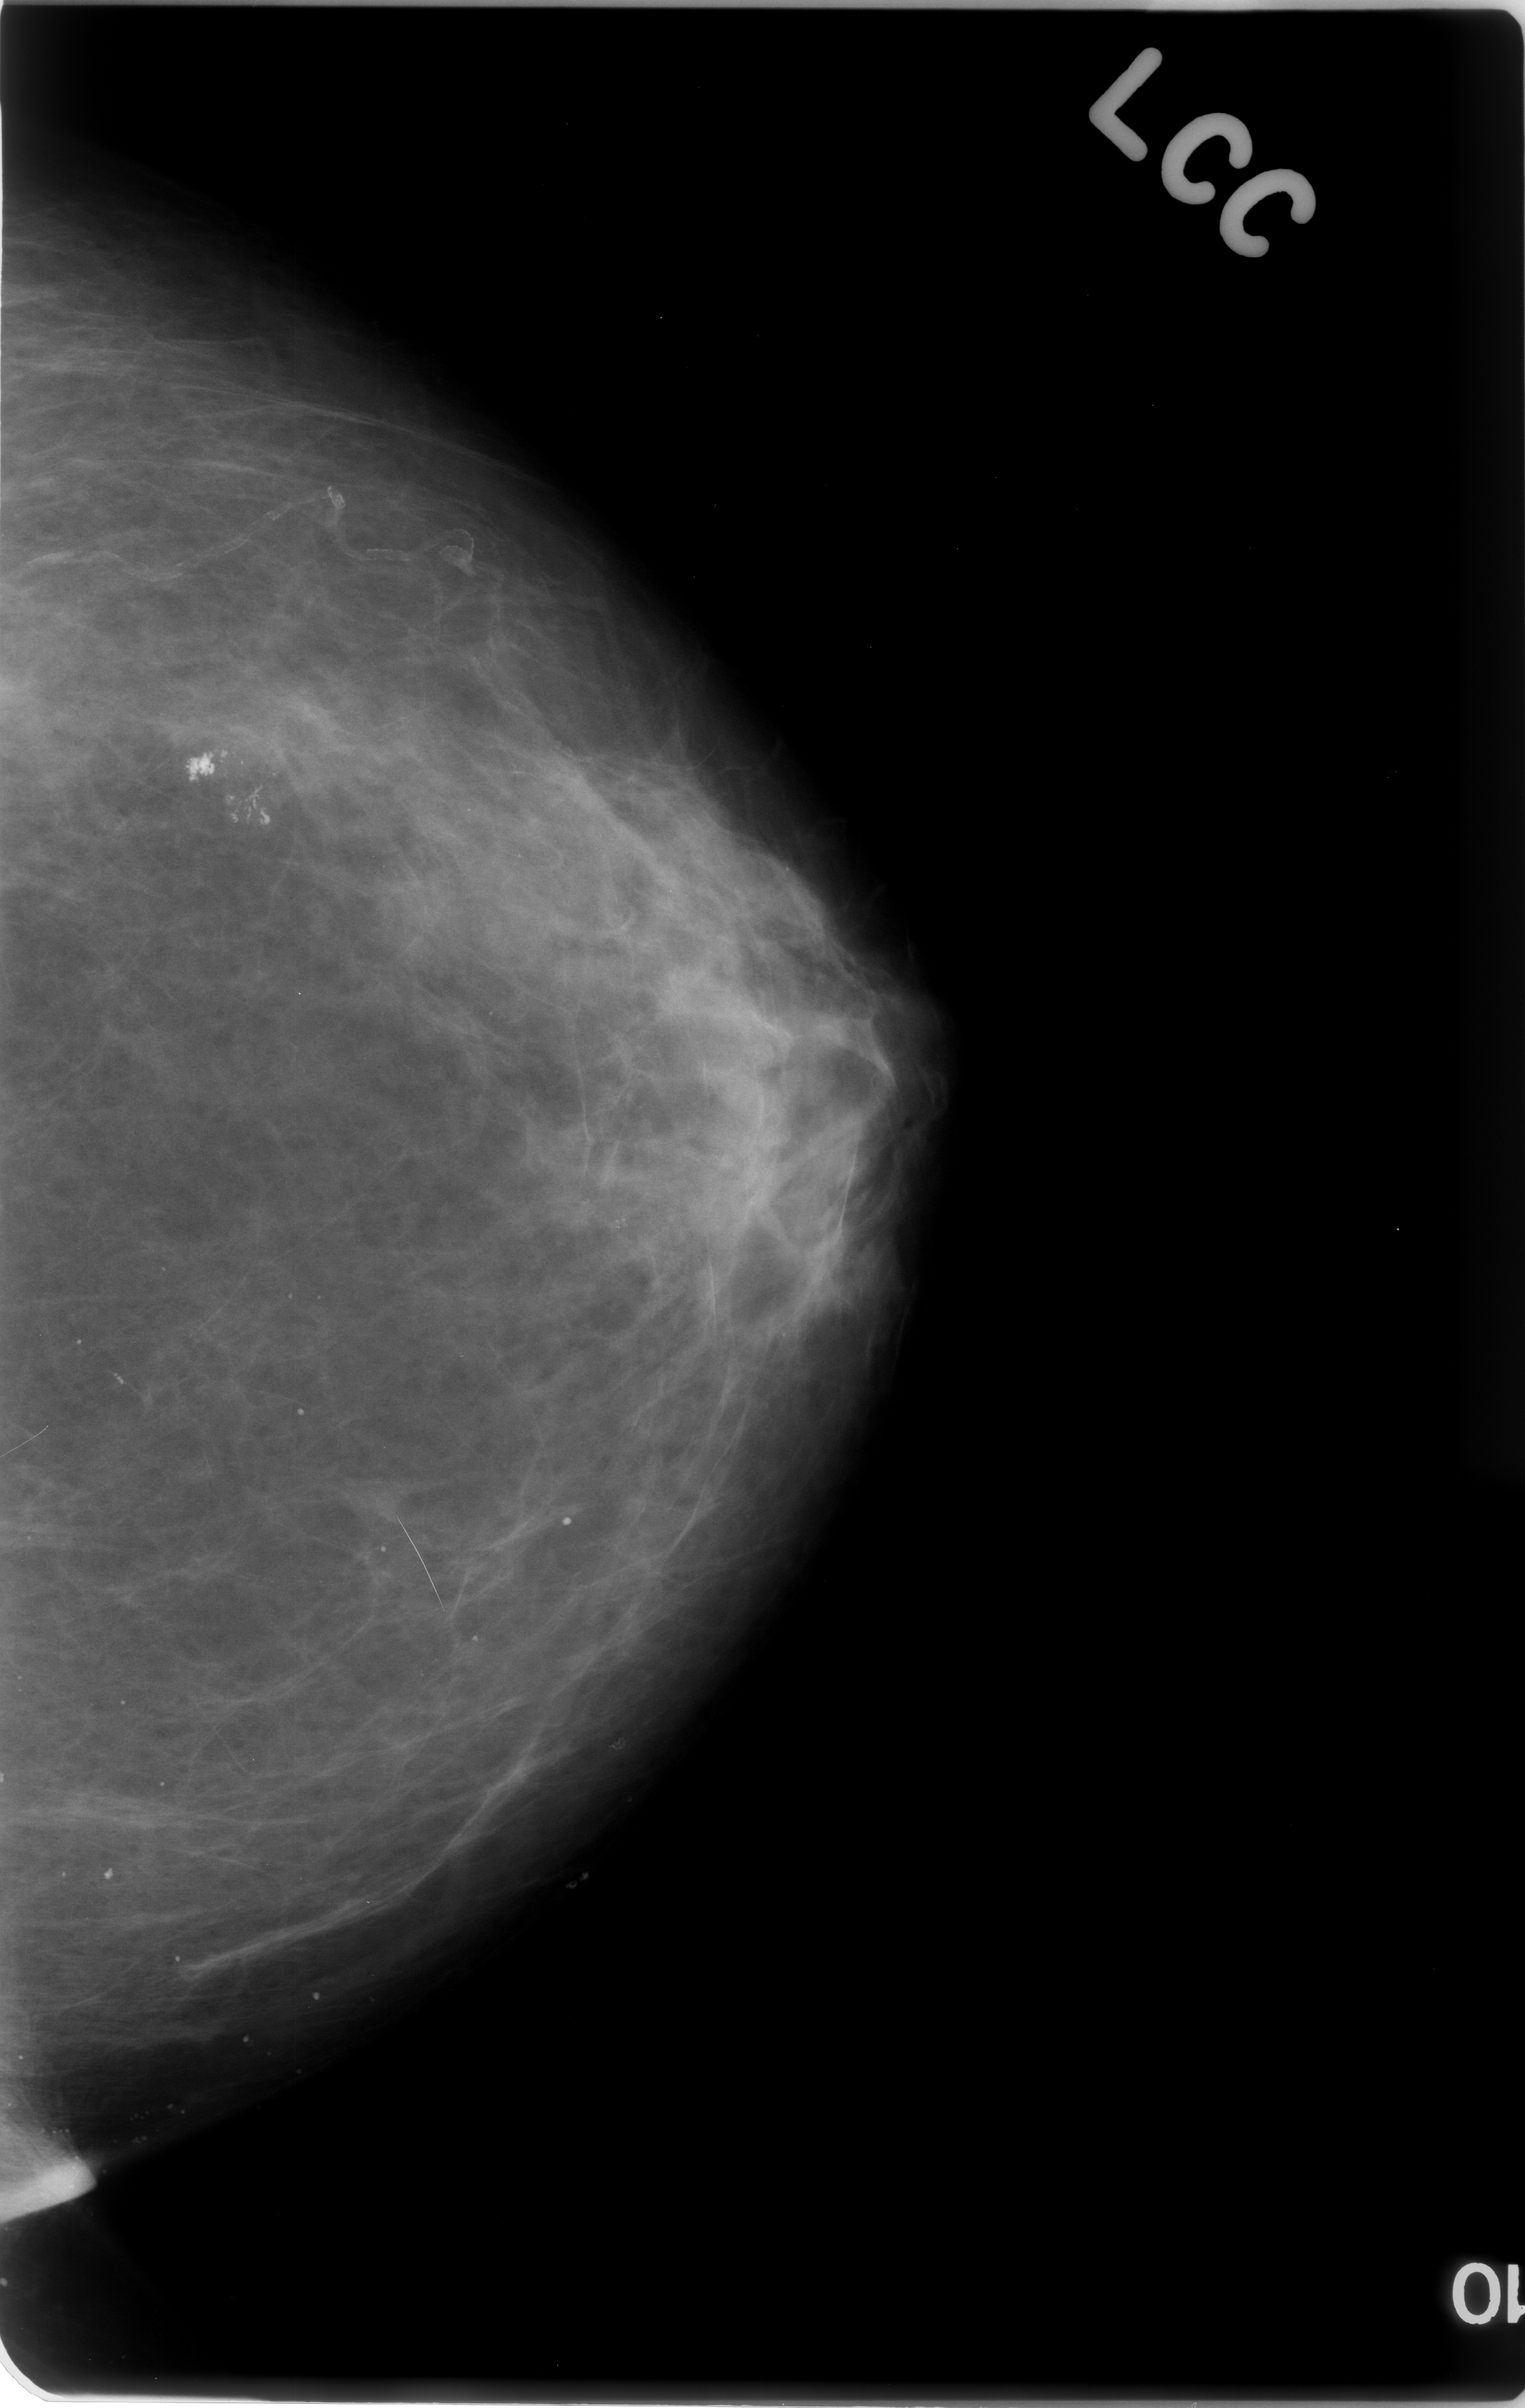
Mammogram (digitized film); left breast; craniocaudal (CC) view; BI-RADS breast density category 1 (scale 1–4); 1525 × 2408 image matrix.
Marked abnormalities (boxes around the expert regions of interest):
- calcifications, morphology pleomorphic / fine linear branching, distribution clustered; BI-RADS assessment category 3; subtlety rating 5 on a 1 (subtle) to 5 (obvious) scale; pathology result (as recorded, not read from the image): benign: bounding box (x1, y1, x2, y2) in pixels: (99, 646, 374, 934)